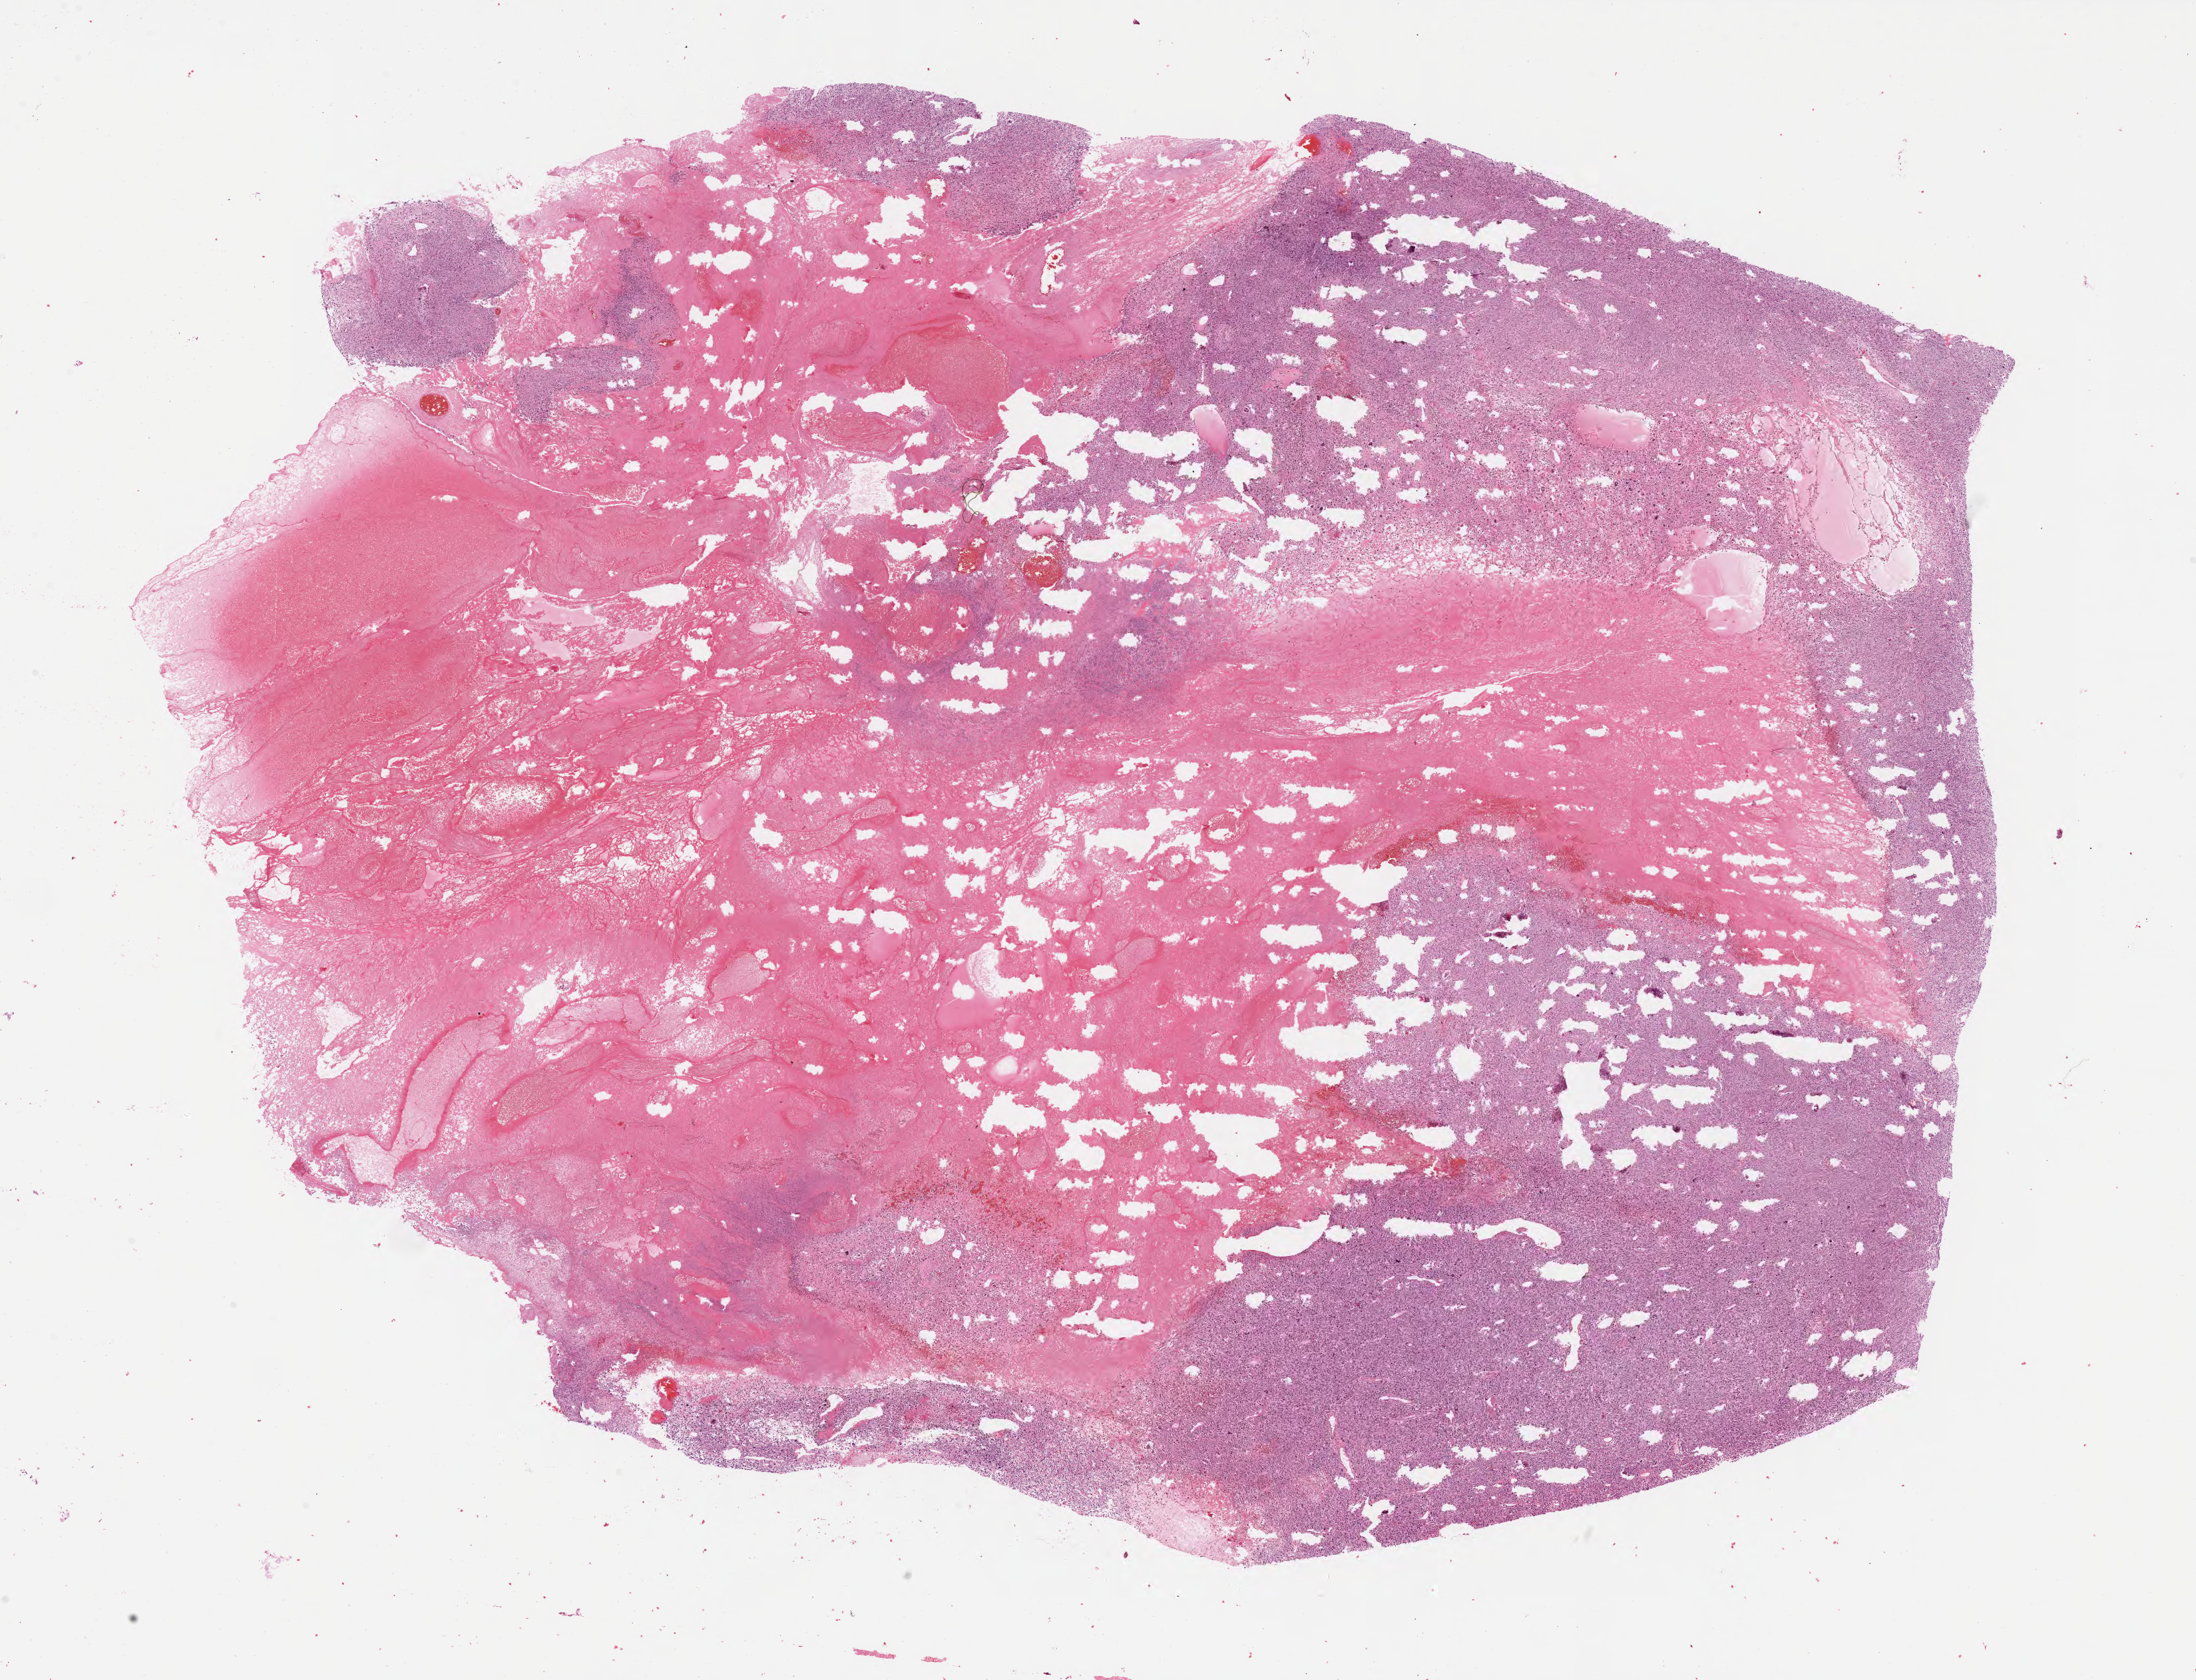
Whole-slide histology image, H&E-stained, a low-resolution overview of the entire scanned area, about 26.0 x 19.9 mm (acquisition: 40x scan). Formalin-fixed paraffin-embedded (FFPE) diagnostic section. Connective, subcutaneous and other soft tissues, primary tumour sample. Male, age 47 years at initial diagnosis.
• histologic diagnosis: Undifferentiated sarcoma (connective, subcutaneous and other soft tissues of lower limb and hip)